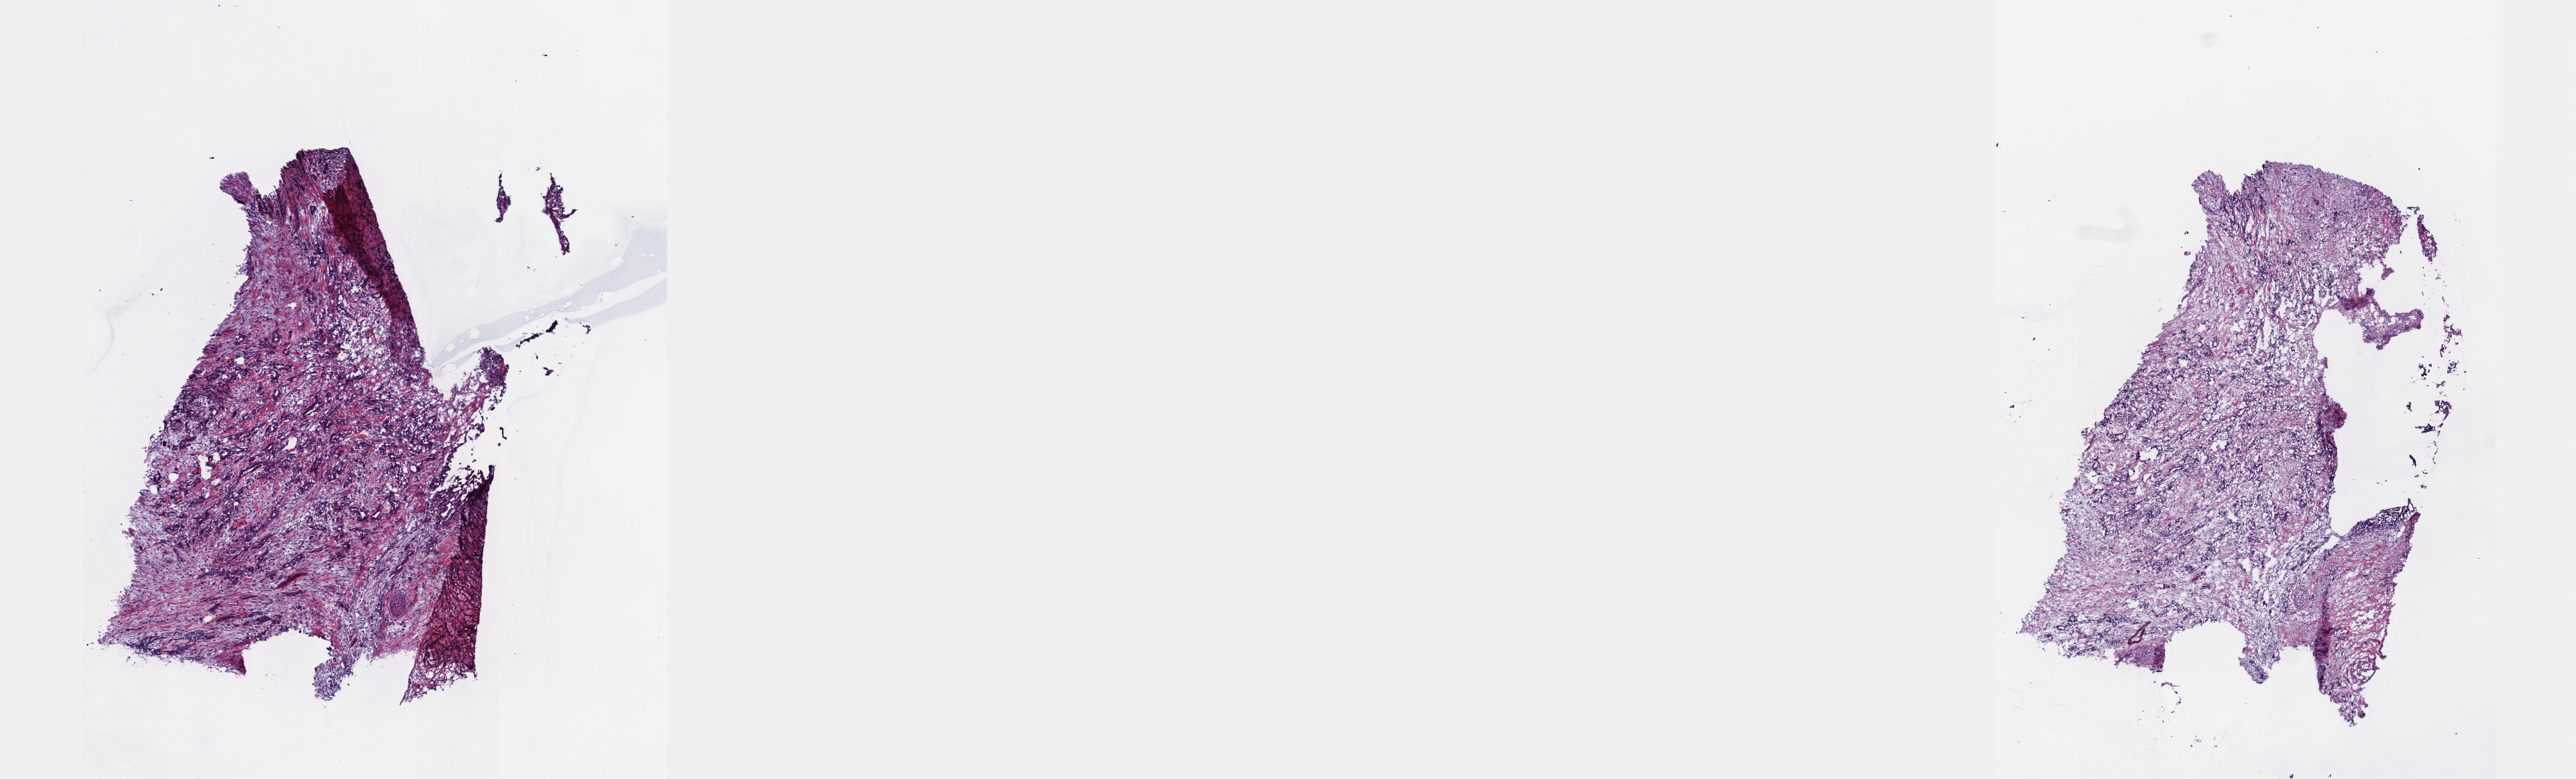
Whole-slide histology image, Hematoxylin and eosin (H&E) stained — a low-resolution overview of the entire scanned area, about 15.6 x 4.7 mm; frozen section; sample: primary tumour, pancreas. Female, age 69 years at initial diagnosis. Histologic grade: G3 (poorly differentiated). Composition of this section per pathologist review: tumour cells 80%, tumour nuclei 80%, normal cells 0%, stromal cells 20%, necrosis 0%. Infiltration values recorded for this section: lymphocyte infiltration 40%, monocyte infiltration 20%, neutrophil infiltration 20%.
Histologic diagnosis: Infiltrating duct carcinoma, NOS (head of pancreas). AJCC pathologic stage: IIB (7th edition). Lymph nodes positive (case pathology): 5 of 21 examined.